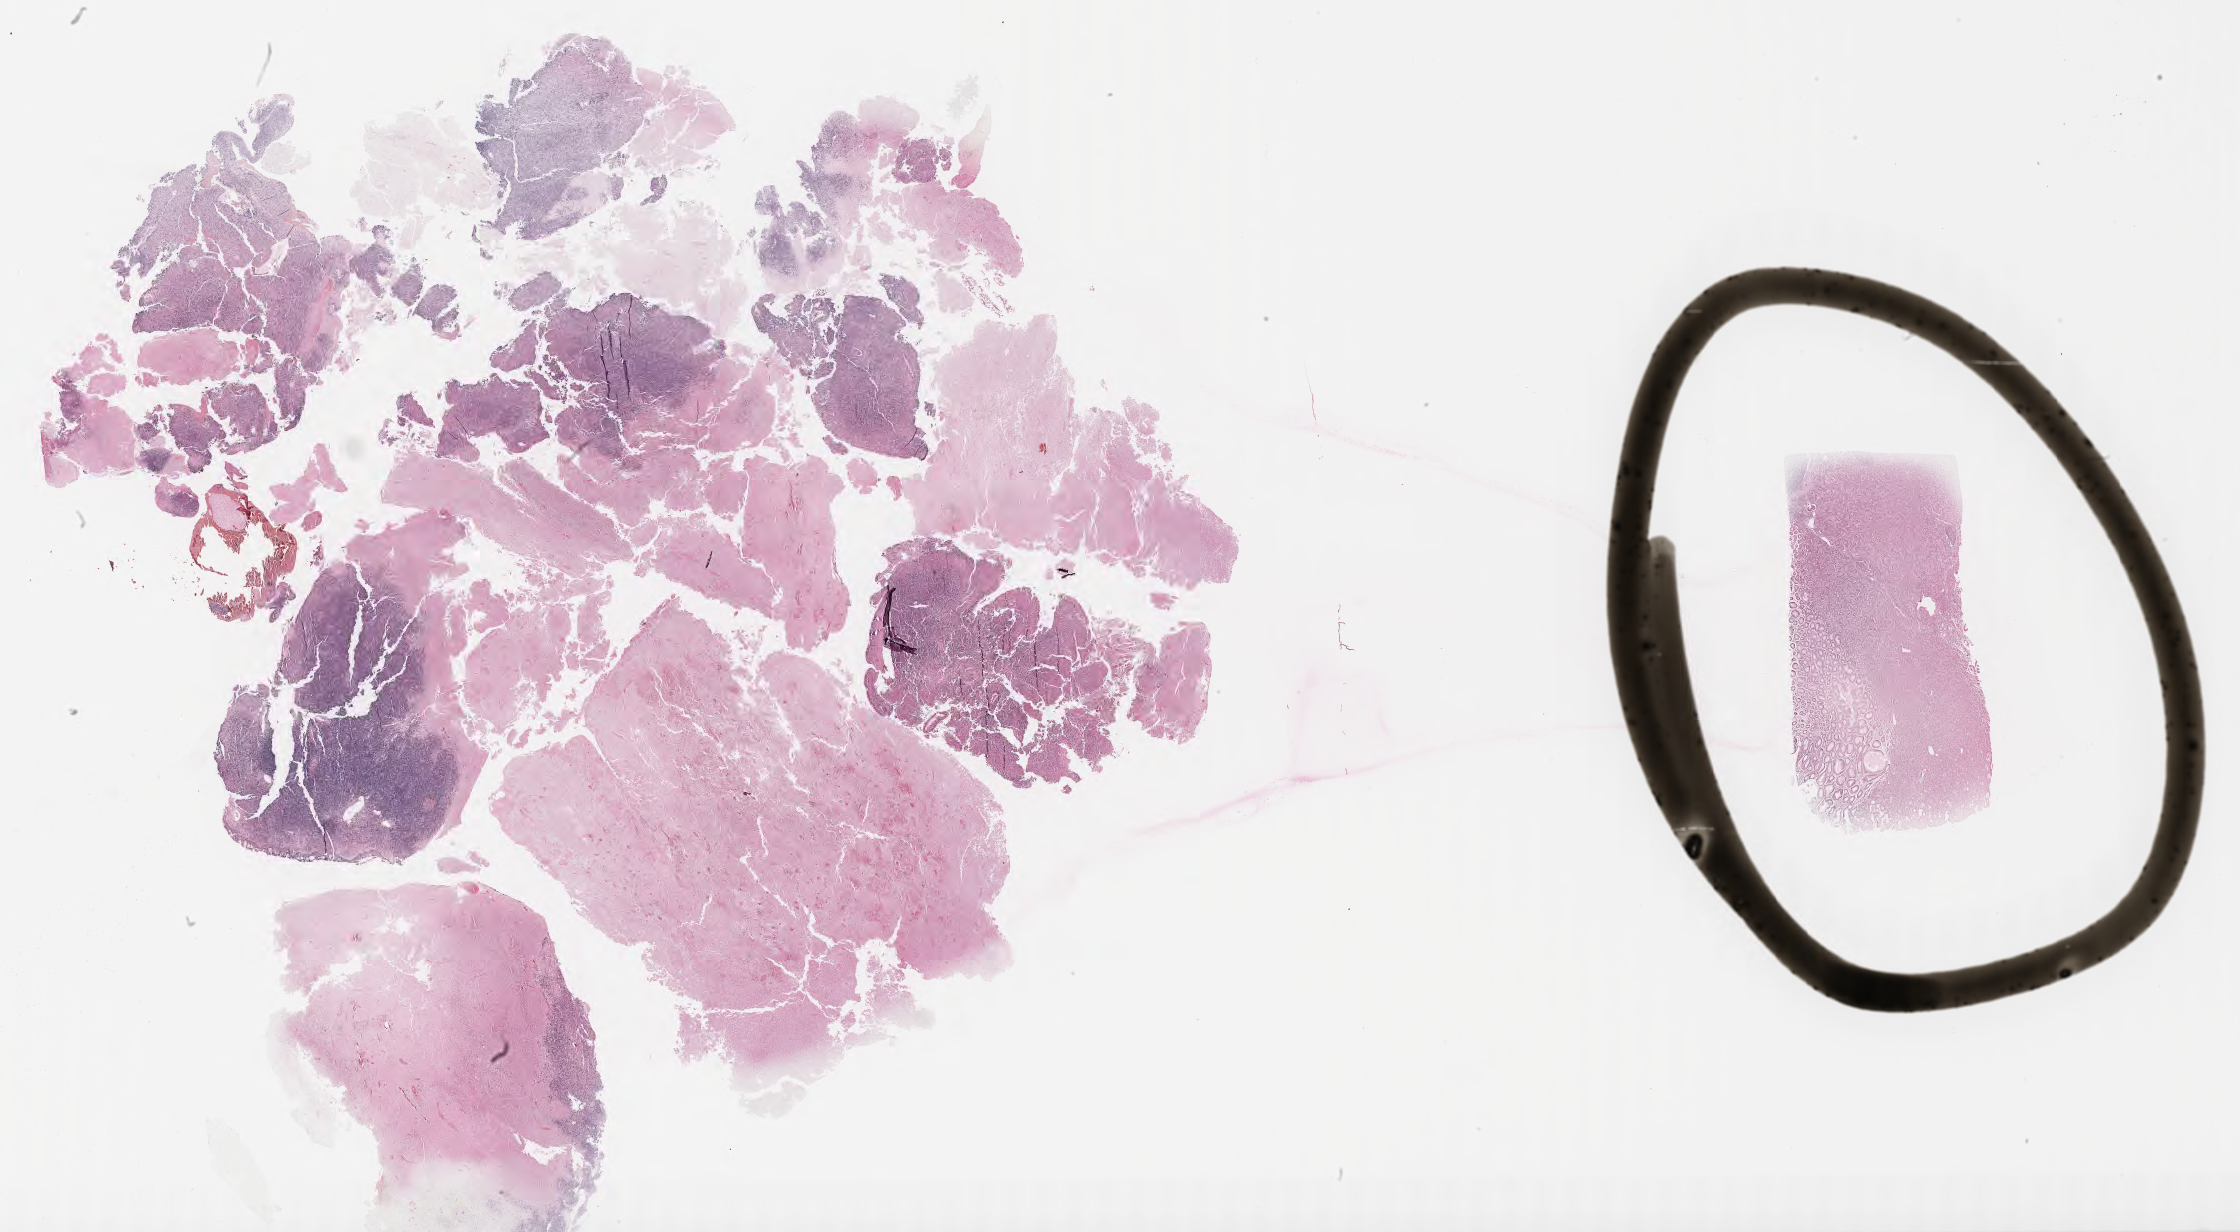
Whole-slide image; stain recorded as Iodonitrotetrazolium — a low-resolution overview of the entire scanned area, about 36.2 x 19.9 mm. Specimen: tumor tissue. Patient male; aged 47.
Histologic diagnosis: Diffuse large B-cell lymphoma, NOS.